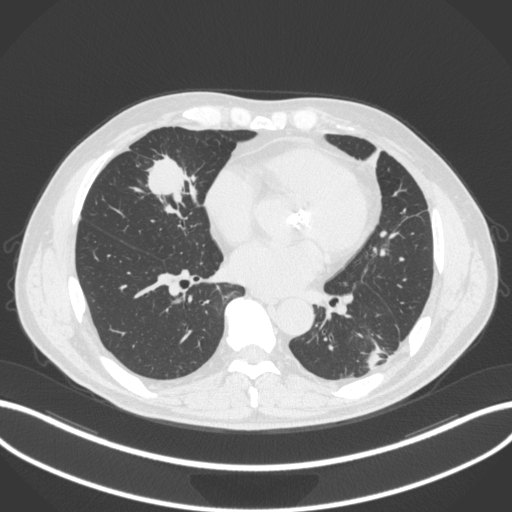
Chest CT, one axial slice. Slice 120 of 399 in the series (ordered by position). Lung window (W 1500 / L -600 HU). 1 mm slice thickness. 512 × 512 image matrix. Male patient, age 59 years. Case-level facts recorded for this patient, not image findings: clinical TNM (as recorded): T2a N1 M0.
Structures marked on this image (bounding box drawn by a radiologist):
- lung tumour (recorded histology: adenocarcinoma): box from (x=133, y=149) to (x=201, y=216) px